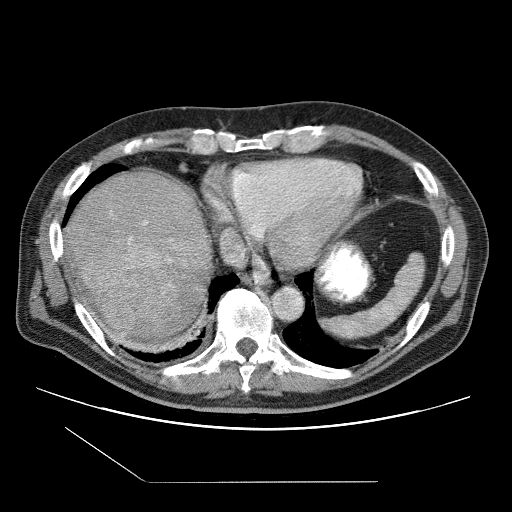
Contrast-enhanced abdominal CT (liver protocol), one axial slice. Slice 91 of 109 in the series (ordered by position). One of 2 acquisitions stored at this slice position. Soft-tissue window (W 400 / L 40 HU). 2.5 mm slice thickness. 512 × 512 image matrix, field of view 400 × 400 mm. Case-level facts recorded for this patient, not image findings: diagnosis: hepatocellular carcinoma (patient treated with transarterial chemoembolisation; whether this scan precedes or follows treatment is not stated here); TNM stage (as recorded): Stage-IIIB; Child-Pugh class: A; tumour differentiation: well differentiated.
Outlined on this slice (semi-automatically segmented with operator editing):
- liver parenchyma outside the tumour (the mass and vessels are separate outlines, so this box may not span the whole liver): bounding box (x1, y1, x2, y2) in pixels: (64, 170, 210, 350)
- mass: (71, 228, 180, 330)
- liver vessels: (143, 222, 173, 261)